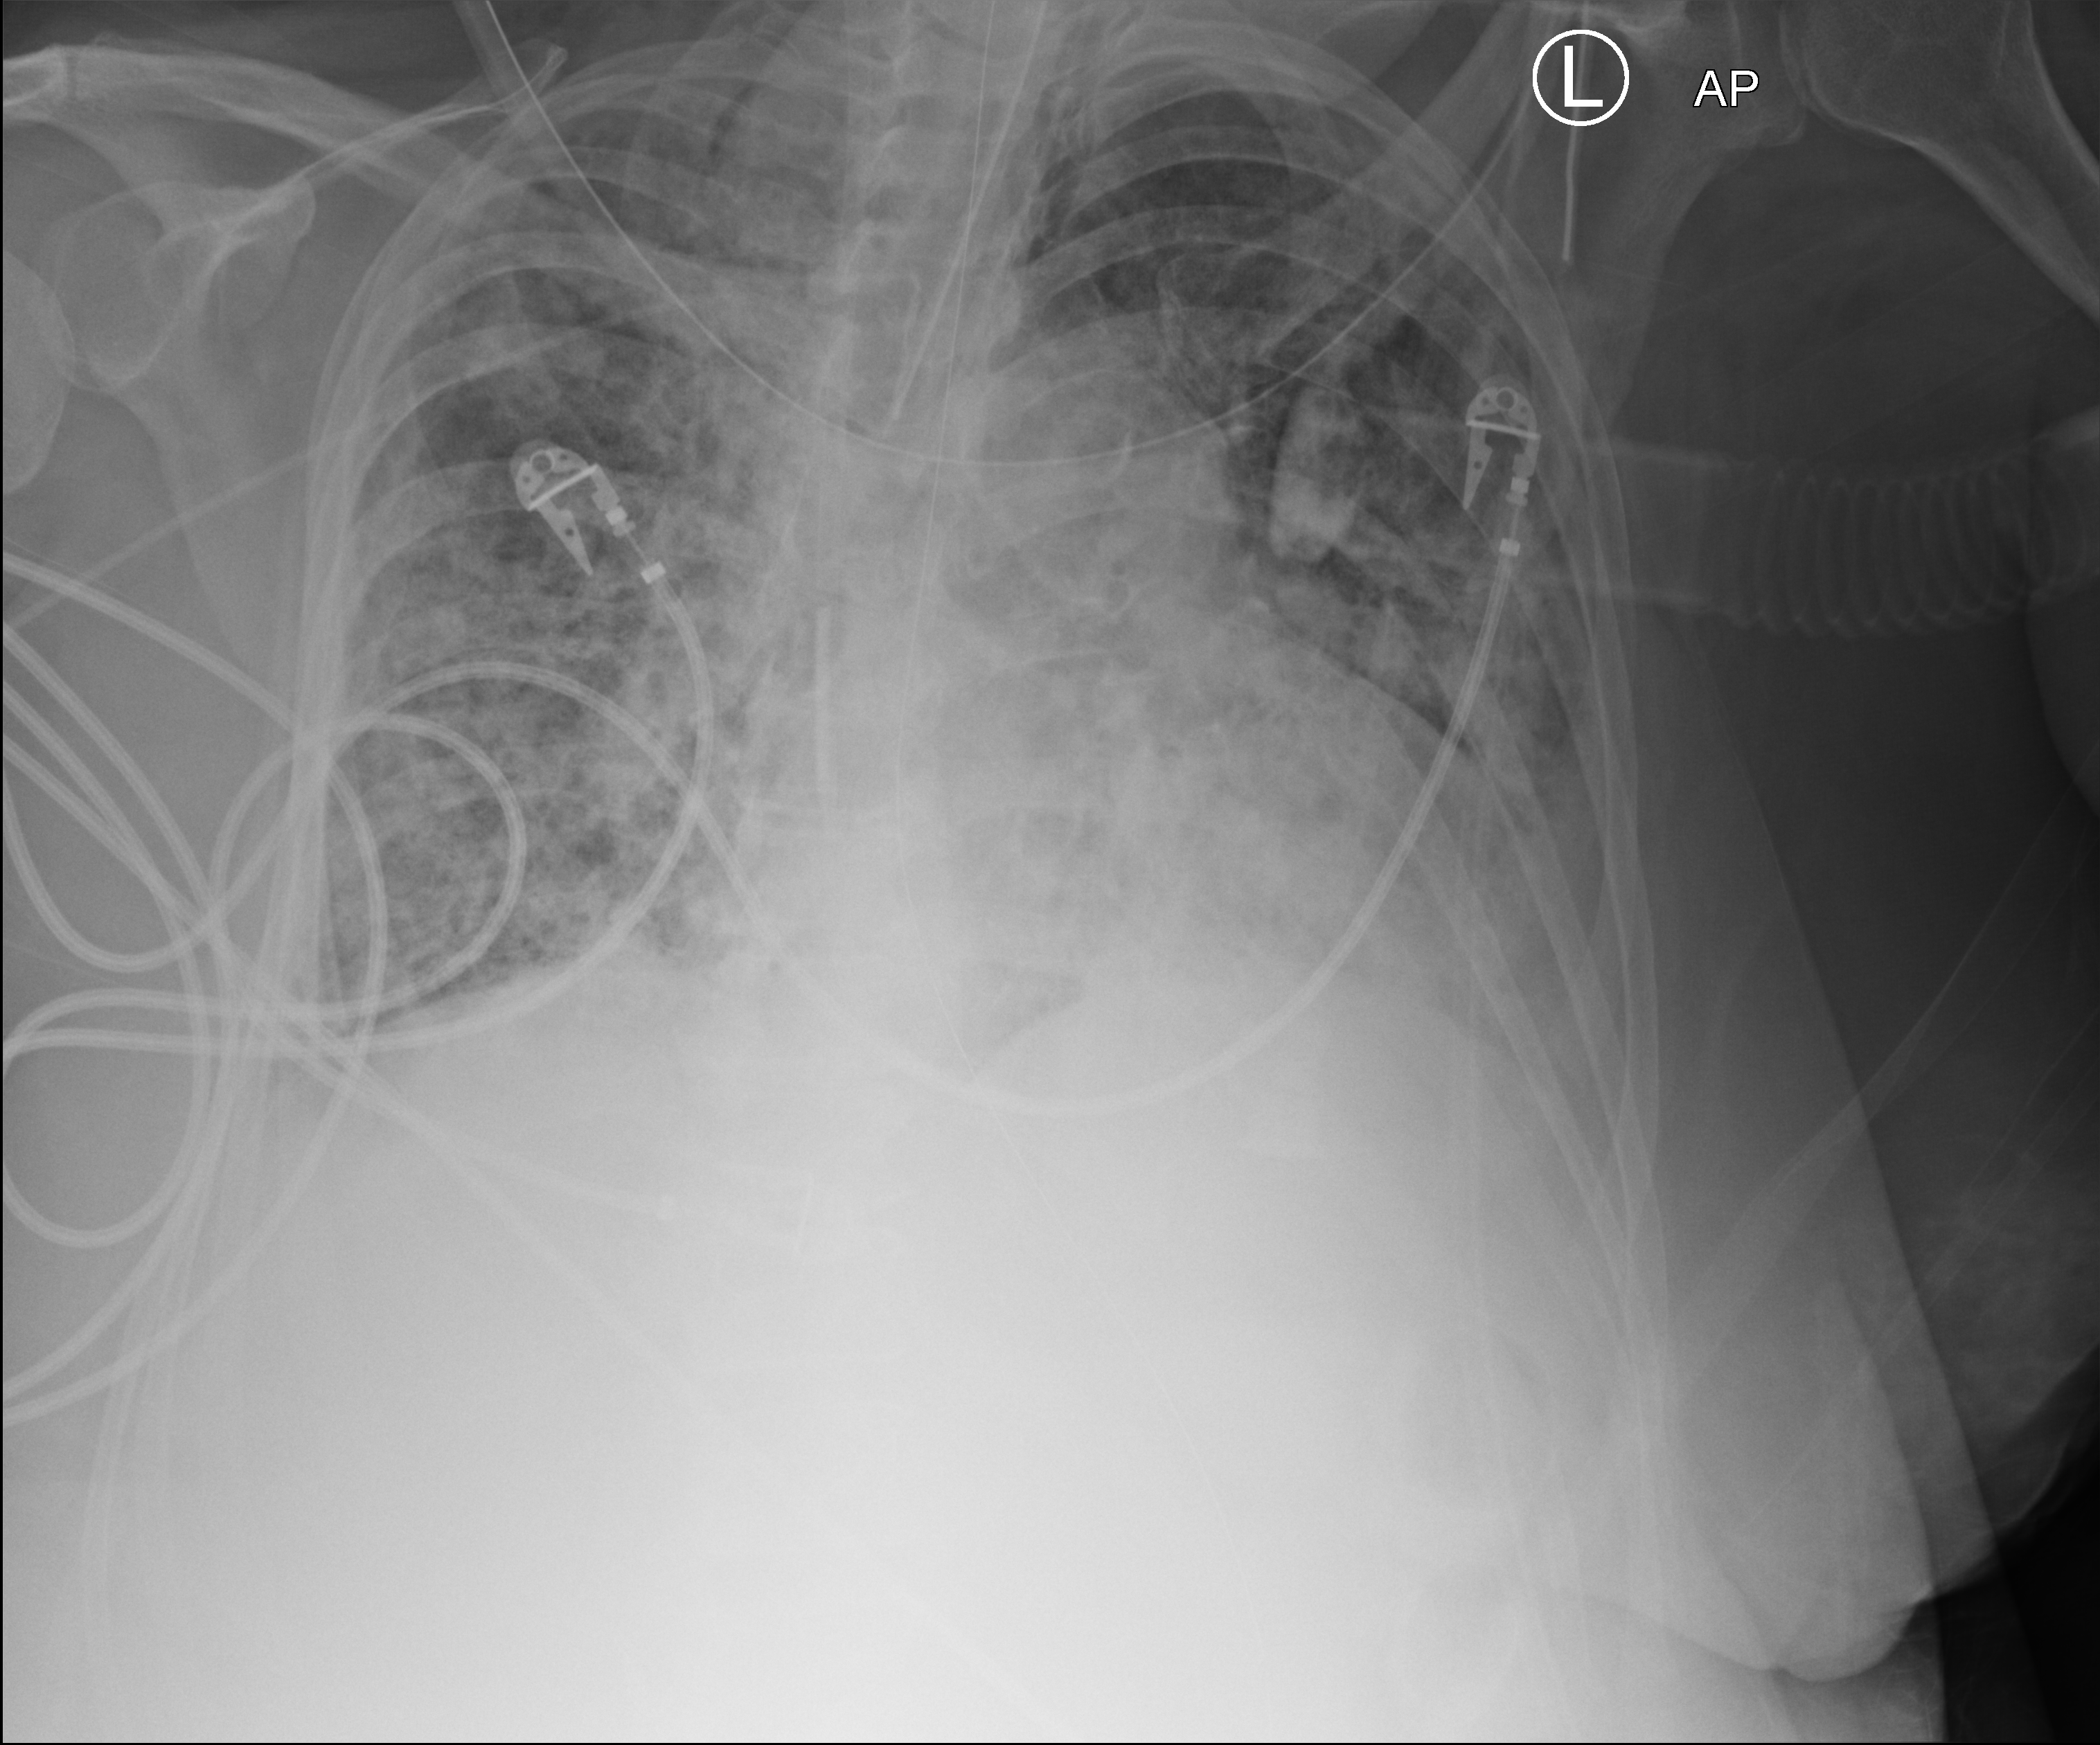
Bedside chest radiograph (computed radiography), anteroposterior (AP) projection. Female patient hospitalised with COVID-19, age 60–74 years.
Admission-level facts for this patient (not findings on this image; timing relative to this image not recorded): hypertension (admission record): yes.